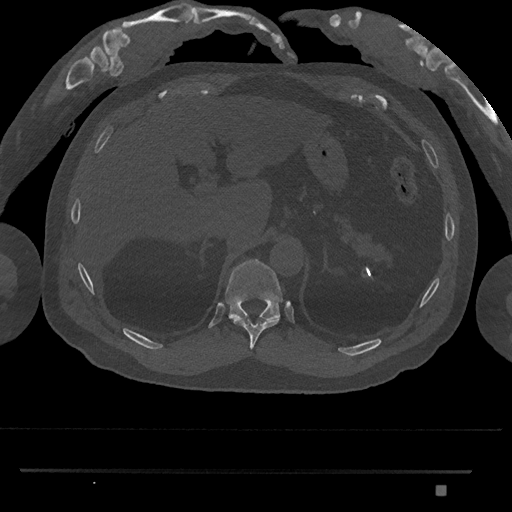
CT including the spine, one axial slice. Slice 972 of 1134 in the series (ordered by position). Reconstruction kernel Br40s/3. Bone window (W 1800 / L 400 HU). 0.5 mm slice thickness. 512 × 512 image matrix, field of view 429 × 429 mm. Male patient, age 65 years. Case-level facts recorded for this patient, not image findings: primary cancer: prostate.
Outlined on this slice (semi-automatically segmented with operator editing):
- T10 vertebra: bounding box <230,317,280,350> (left, top, right, bottom; pixels)
- T11 vertebra: <225,259,283,320>